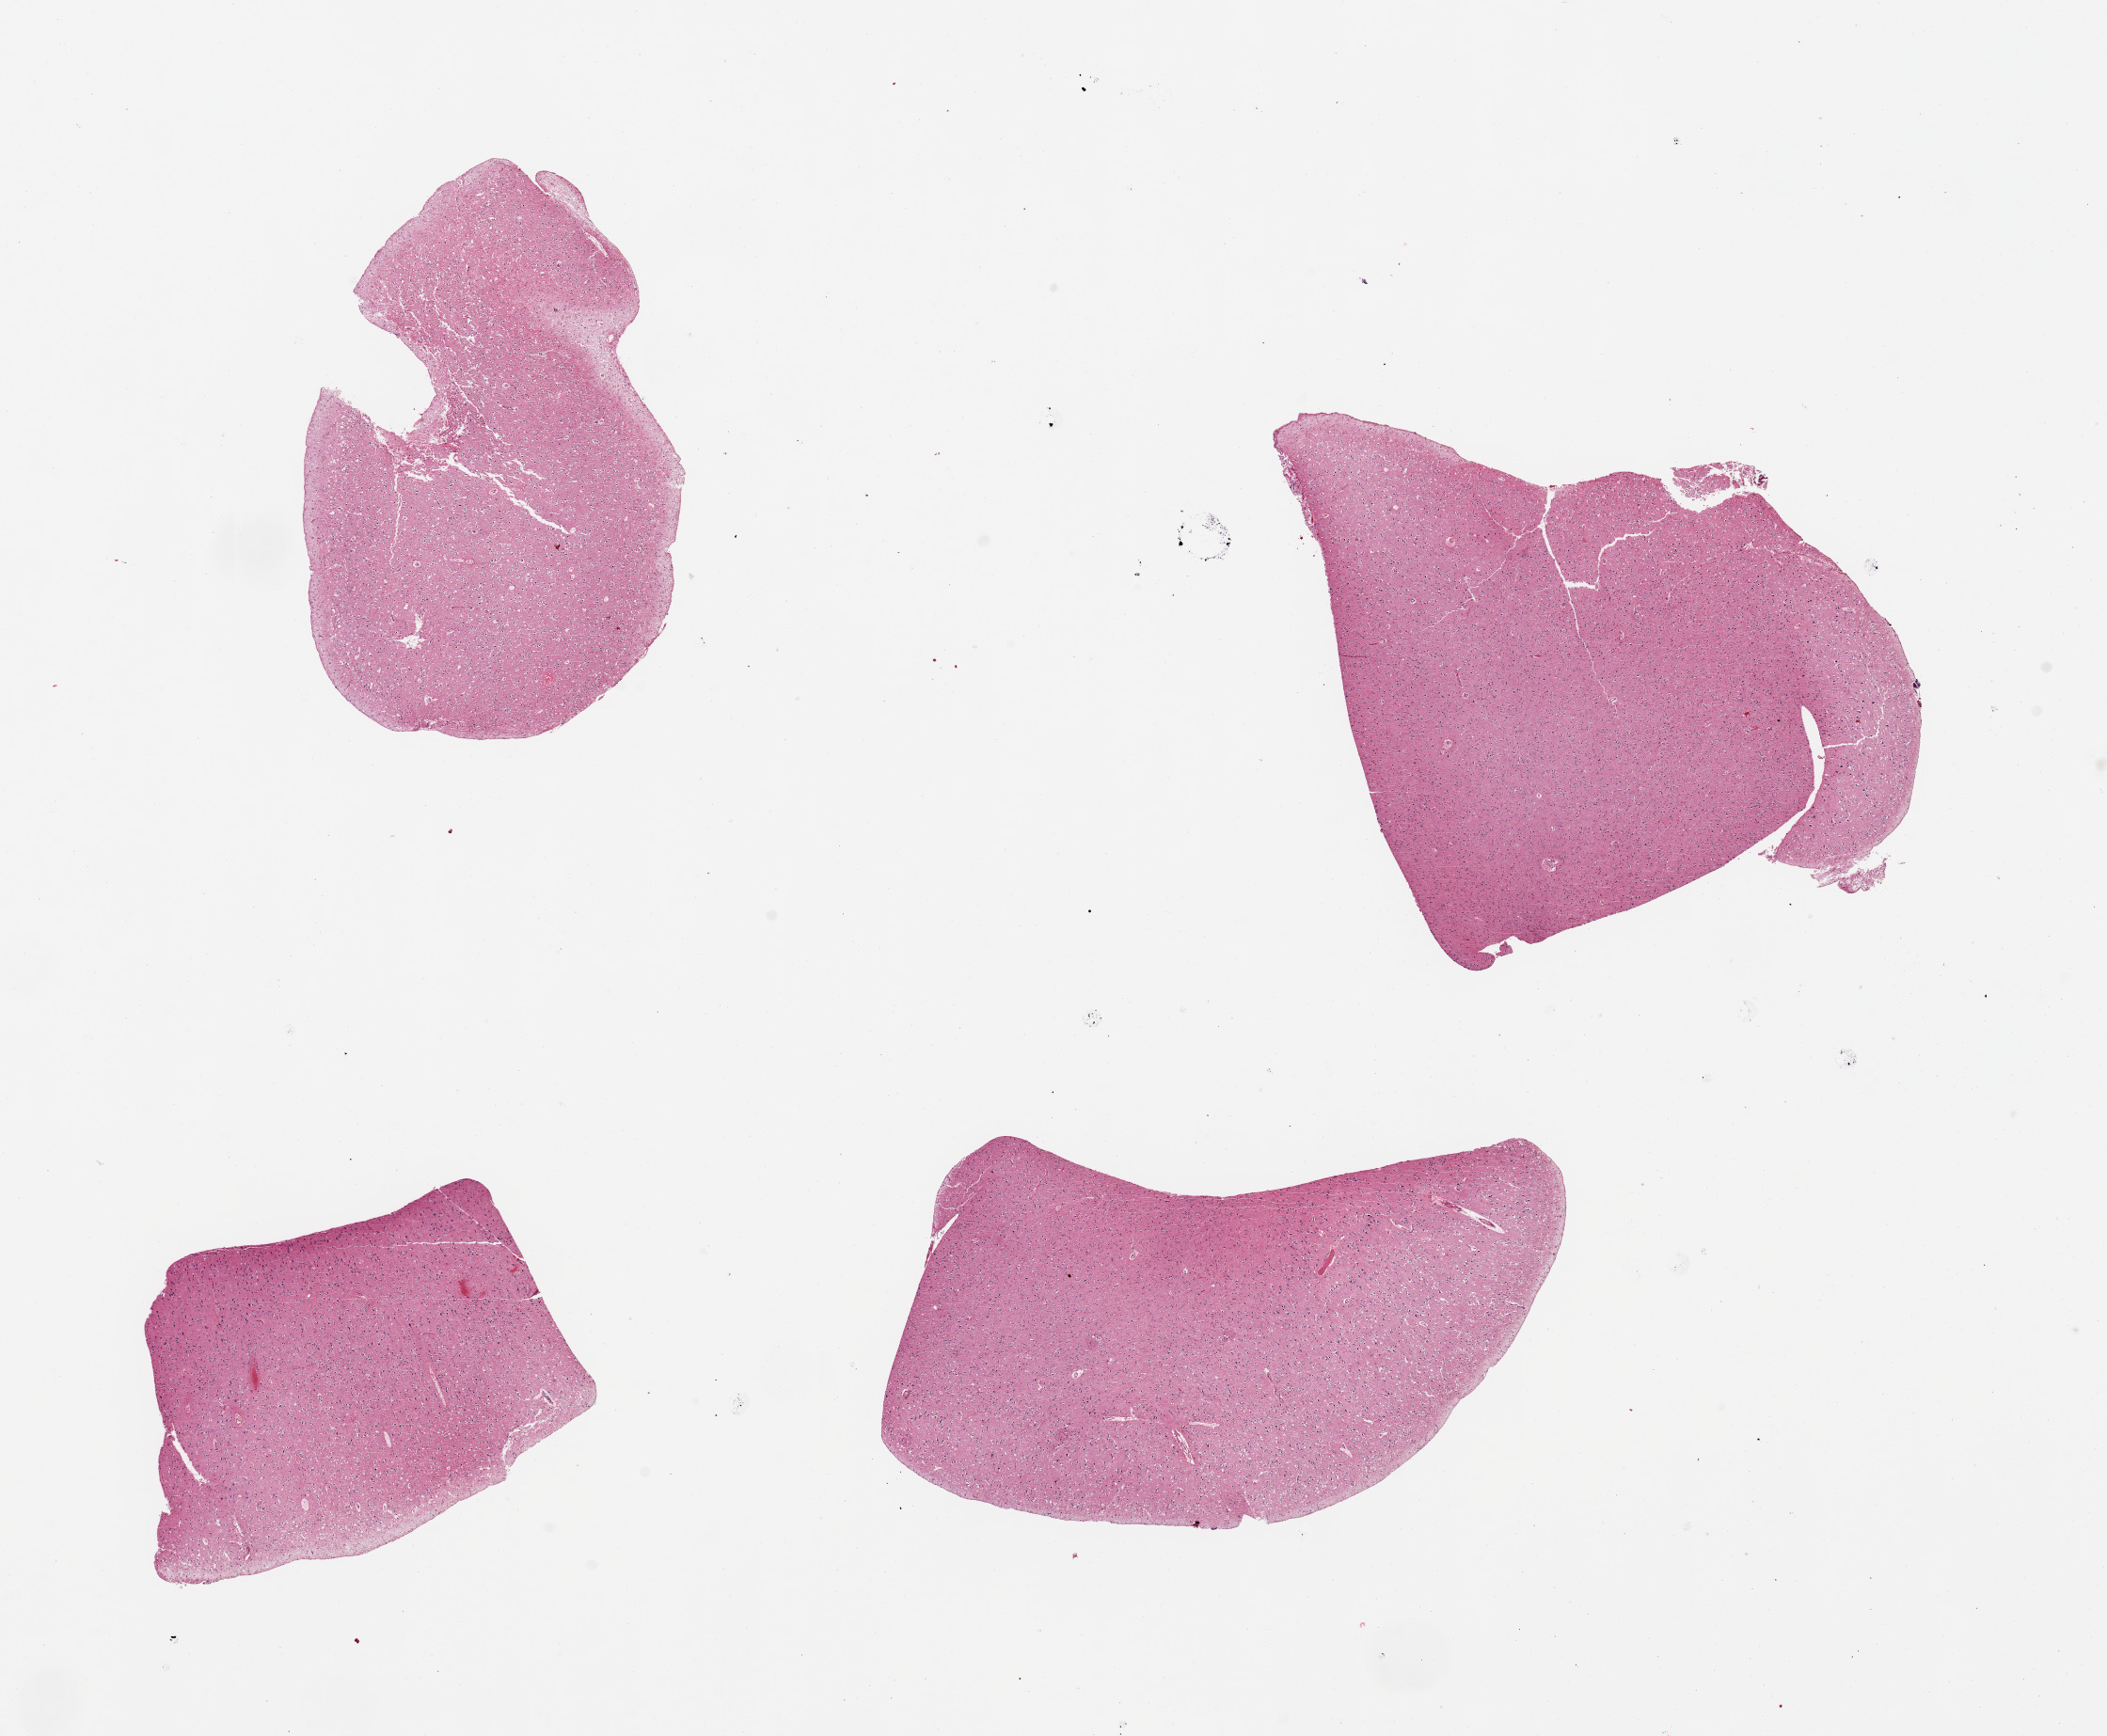
Digitized hematoxylin and eosin (H&E)-stained section, brightfield, a low-resolution overview of the entire scanned area, about 17.7 x 14.6 mm (acquisition: 20x scan); PAXgene-fixed paraffin-embedded (PFPE) section; target tissue: cerebral cortex; tissue donor sample. Donor: male.
Review note (as recorded): 4 pieces, no abnormalities.